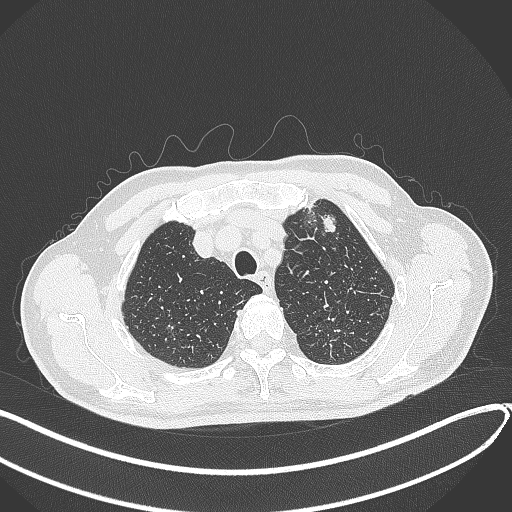
Chest CT, one axial slice; position 355 of 459 along the scan axis; reconstruction kernel B70f; 120 kVp; lung window (W 1500 / L -600 HU); 1 mm slice thickness; 512 × 512 image matrix, field of view 400 × 400 mm. Patient: male, 74 years. From the clinical record (not read from this slice): clinical TNM (as recorded): T2b N0 M1c.
Structures marked on this image (bounding box drawn by a radiologist):
- lung tumour (recorded histology: adenocarcinoma): bounding box [x1, y1, x2, y2] px = [320, 211, 337, 236]